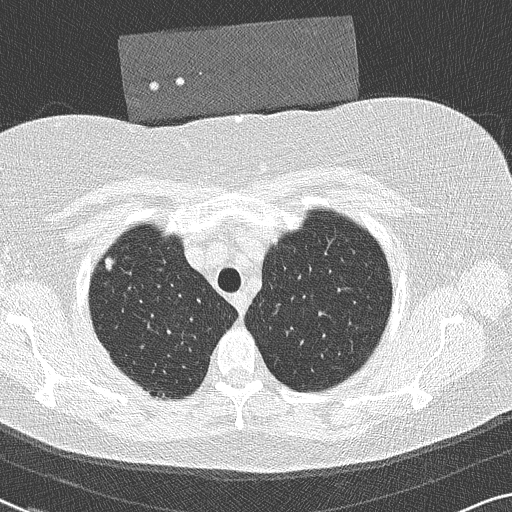
Chest CT (low-dose screening protocol), one axial image, baseline annual screen, lung window (W 1500 / L -600 HU), 2 mm slice thickness, lung (sharp) reconstruction kernel (B50f), 512 × 512 image matrix, field of view 330 × 330 mm. Female, age 58 years at enrolment. Former smoker at enrolment.
• Expert-annotated lung lesion, box from (x=91, y=246) to (x=131, y=292) px.
• No non-calcified nodule or mass ≥4 mm was recorded by the screening reader at this exam.
• Official screen result: negative screen, minor abnormalities not suspicious for lung cancer.